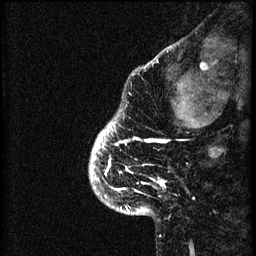
Breast MRI (dynamic contrast-enhanced), one sagittal slice; position 7 of 60 along the scan axis; 3 images stored at this slice position (order not interpretable as contrast timing); 1.5 T; TE 4.2 ms, TR 8.2 ms; 2 mm slice thickness; 256 × 256 image matrix, field of view 180 × 180 mm. Female patient, age 41 years.
Annotated regions visible in this slice (semi-automatically segmented with operator editing):
- analysis volume of interest (the breast-tissue region the enhancement analysis was run in; not a lesion): bounding box (x1, y1, x2, y2) in pixels: (91, 114, 168, 205)
- tumour enhancement mask (voxels above the 70 % enhancement threshold inside the analysis volume of interest): (91, 124, 168, 199)